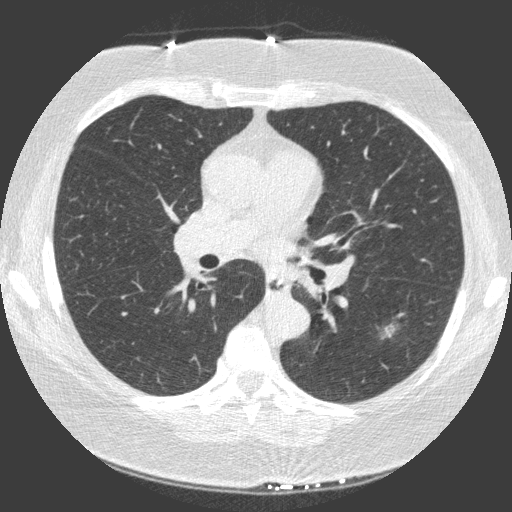
Axial slice from a low-dose chest CT screening exam; third screening round (two years after baseline); lung window (W 1500 / L -600 HU); 1 mm slice thickness; 120 kVp; slice 59 of 149 in the series. Female participant, aged 66 years at enrolment. Current smoker at enrolment.
- Lesion marked by an expert reader, bounding box <366,302,422,351> (left, top, right, bottom; pixels).
- Screening reader's record for this exam (one nodule recorded; not confirmed to be the boxed lesion): non-calcified nodule or mass ≥4 mm, left lower lobe, 23 × 17 mm, spiculated (stellate) margins, soft tissue attenuation, pre-existing on the prior screen: yes; interval growth: yes.
- Official screen result: positive, other.
- Participant outcome: lung cancer diagnosed 15 days after this screen — non-small cell carcinoma, left lower lobe, poorly differentiated (G3), stage IA (AJCC 6th edition), 20 mm at pathology.